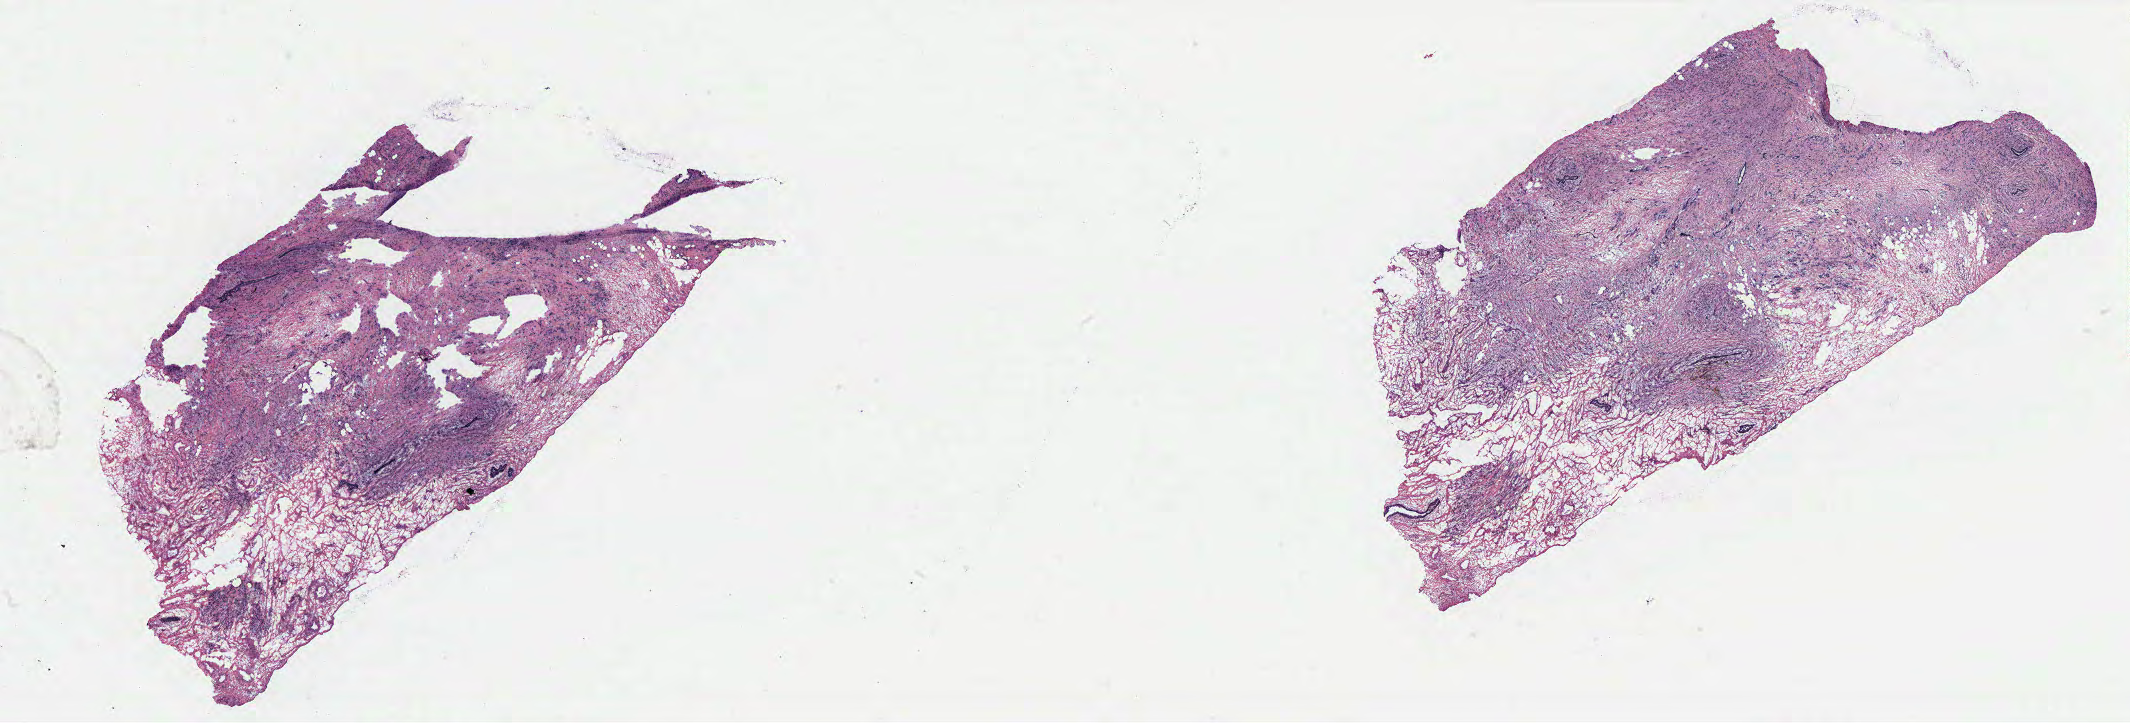
Whole-slide histology image, H&E — low-resolution overview of the scanned area, about 34.1 x 11.6 mm. Breast, tumour tissue. Female, 64 y/o.
AJCC pathologic stage: IIIC. Diagnosis: Infiltrating lobular carcinoma, NOS.